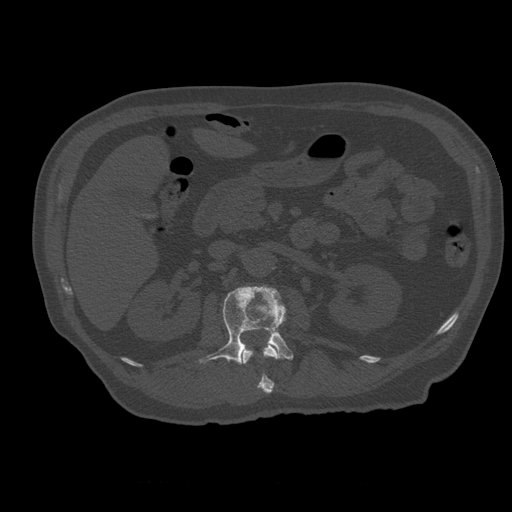
CT including the spine, one axial slice. Position 221 of 399 along the scan axis. Reconstruction kernel STANDARD. 120 kVp. Bone window (W 1800 / L 400 HU). 512 × 512 image matrix. Patient age 73 years. Case-level facts recorded for this patient, not image findings: primary cancer: prostate.
Structures marked on this image (semi-automatically segmented with operator editing):
- L1 vertebra: bounding box <241,344,279,394> (left, top, right, bottom; pixels)
- L2 vertebra: <199,286,294,364>